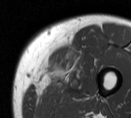
MRI of an extremity soft-tissue mass, one axial slice. Position 14 of 55 along the scan axis. MR volume resampled by the dataset authors to the PET/CT grid (not the native acquisition matrix). 3.27 mm slice thickness. 131 × 118 image matrix, field of view 128 × 115 mm. Male patient. From the clinical record (not read from this slice): histological type: pleiomorphic liposarcoma; grade: high; site of the primary tumour: left thigh.
Outlined on this slice (expert contour drawn on MRI and transferred to this co-registered scan by the dataset authors):
- gross tumour volume including surrounding oedema: bounding box <39,52,90,97> (left, top, right, bottom; pixels)
- gross tumour volume (mass): <39,52,65,83>